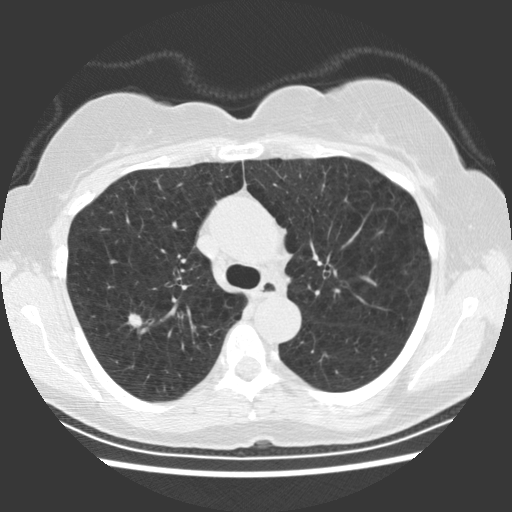
Low-dose screening chest CT, one axial slice. Position 164 of 234 along the scan axis. Reconstruction kernel STANDARD. 120 kVp. Lung window (W 1500 / L -600 HU). 2.5 mm slice thickness. 512 × 512 image matrix.
Structures marked on this image (outlined manually by an expert reader):
- lesion 1 (tumor, upper lobe of right lung): bounding box (x1, y1, x2, y2) in pixels: (128, 313, 143, 328)